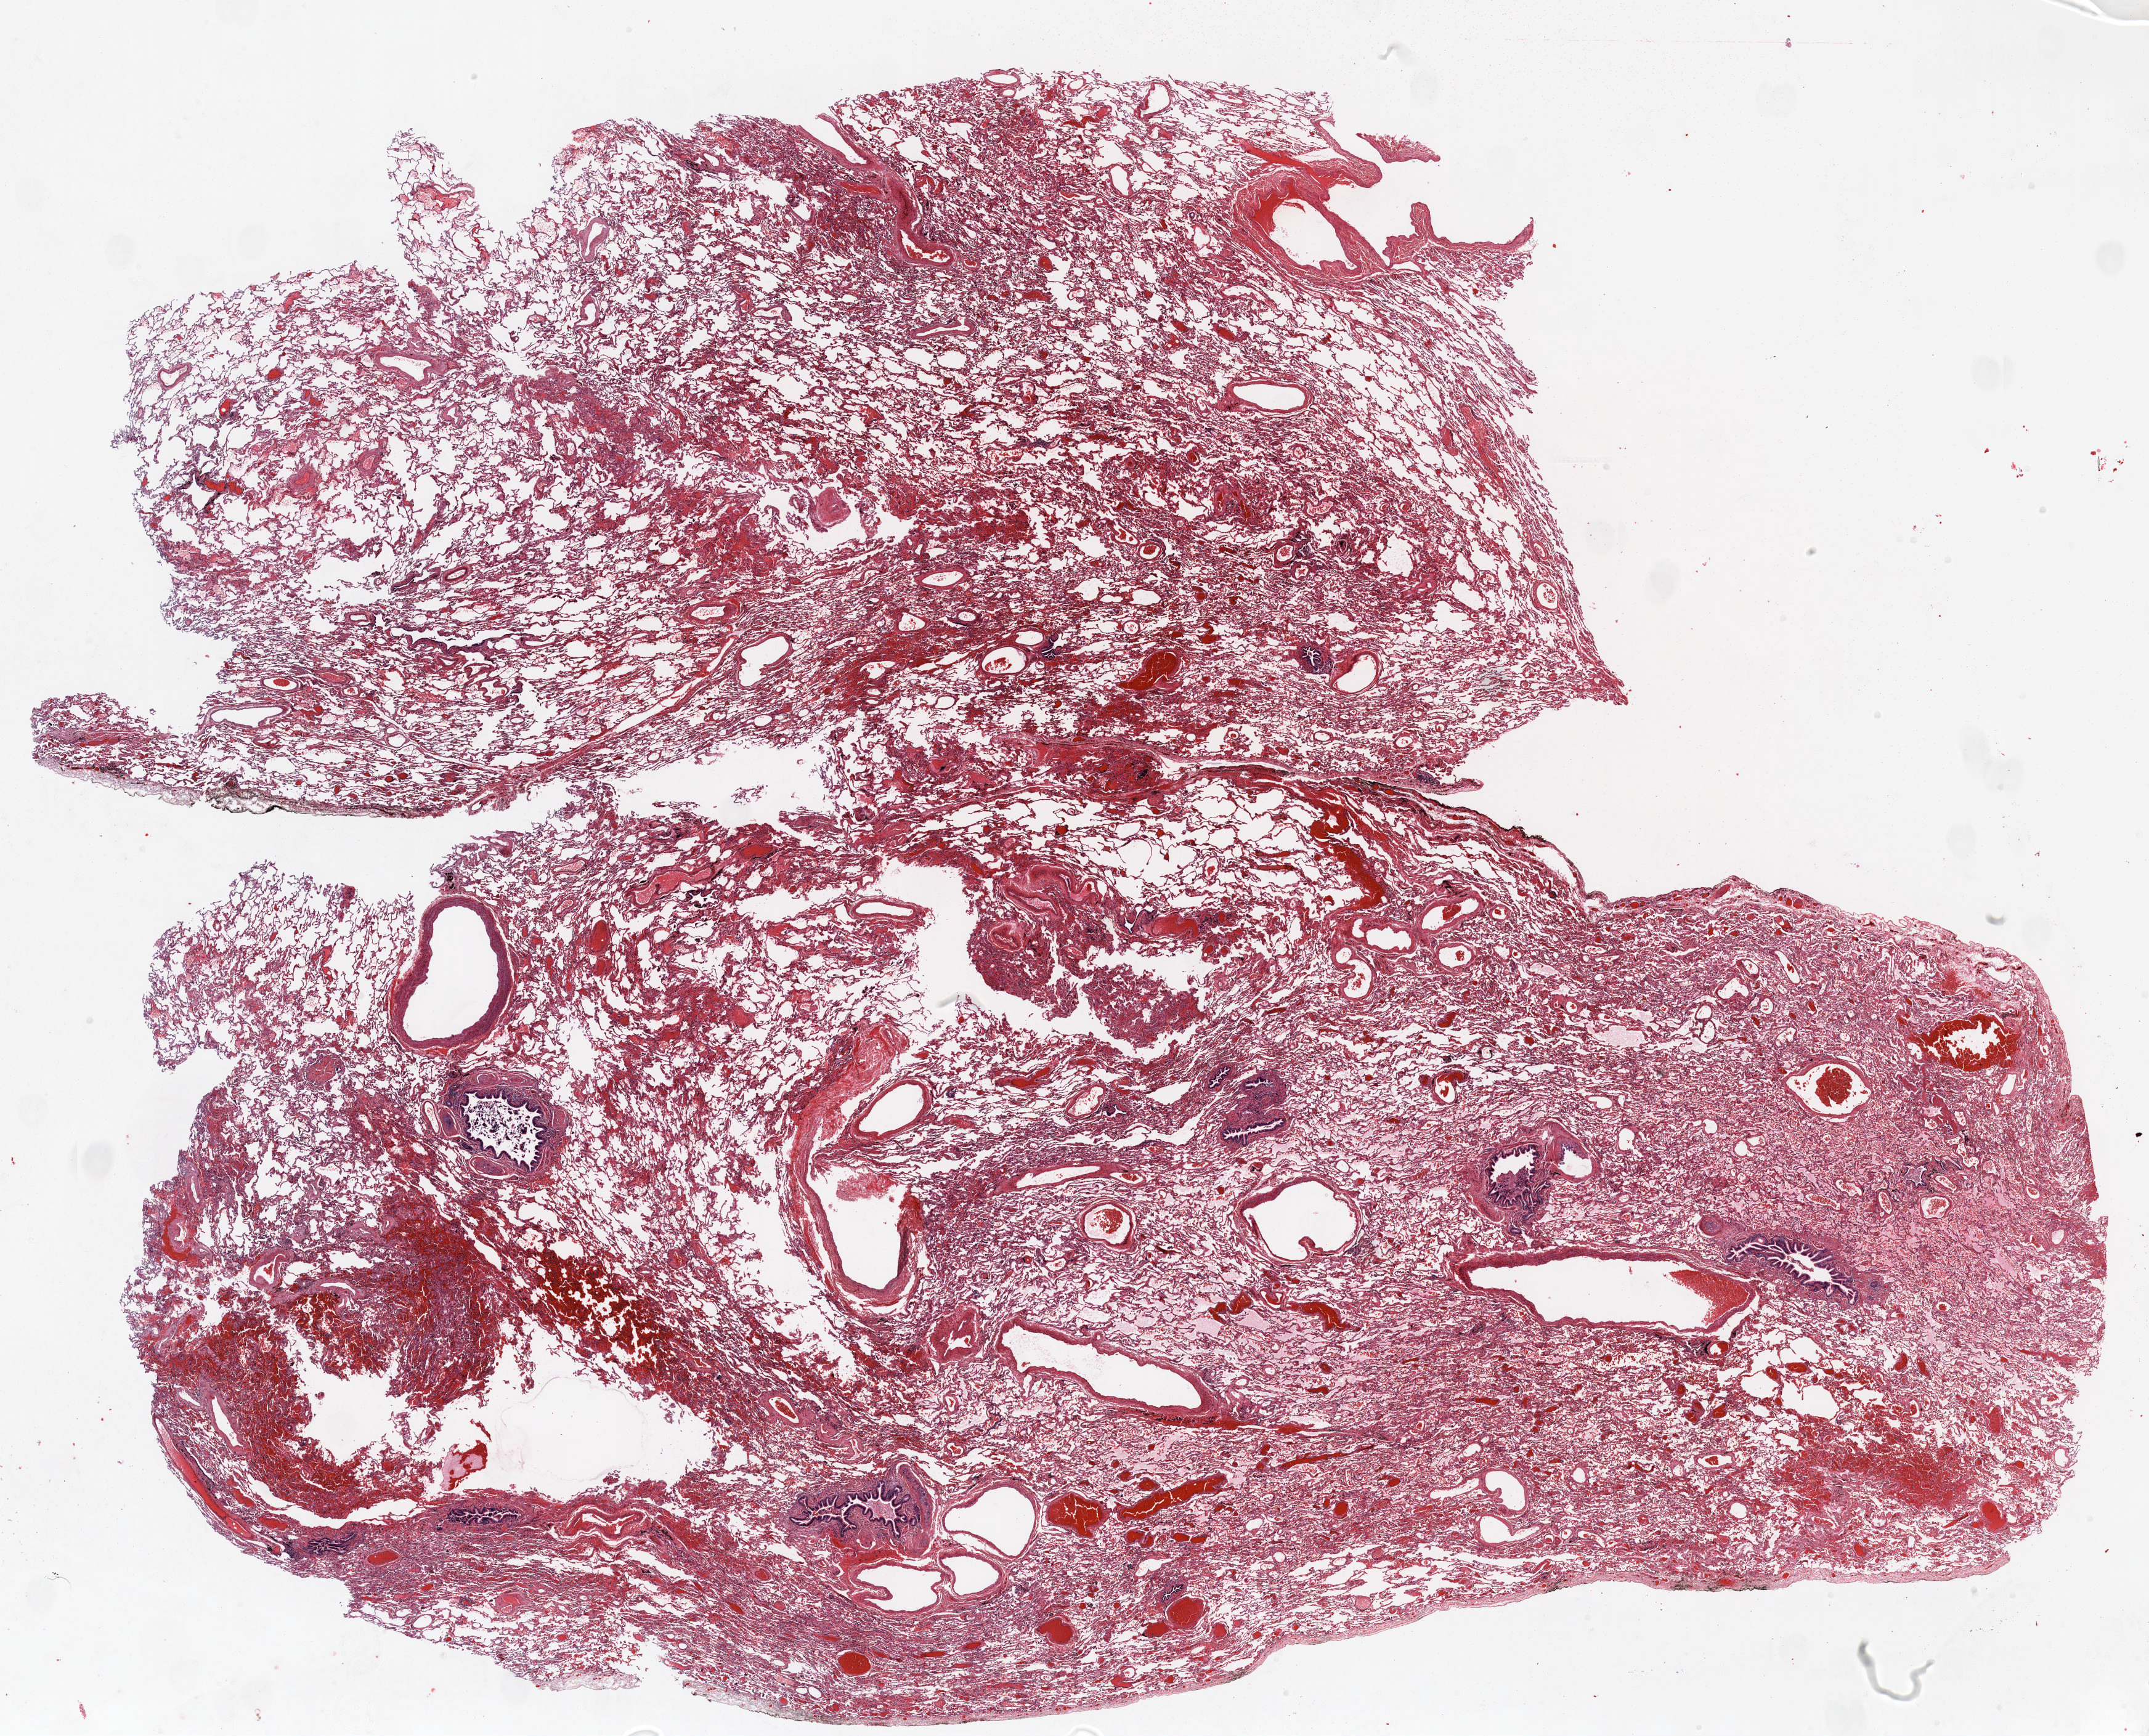
Whole-slide histology image, H&E-stained — low-resolution overview of the scanned area, about 28.0 x 22.6 mm (slide scanned at 20x). Formalin-fixed paraffin-embedded (FFPE) section. Lung tissue. Female, age 61 at enrolment. Former smoker at enrolment. Grade: well differentiated (G1).
- tumour size (pathology): 10 mm
- ICD-O-3 topography: lower lobe of lung (C34.3)
- stage (AJCC 6th edition): IA
- participant's lung-cancer diagnosis: Bronchiolo-alveolar adenocarcinoma, NOS
- primary tumour location (clinical record): left lower lobe